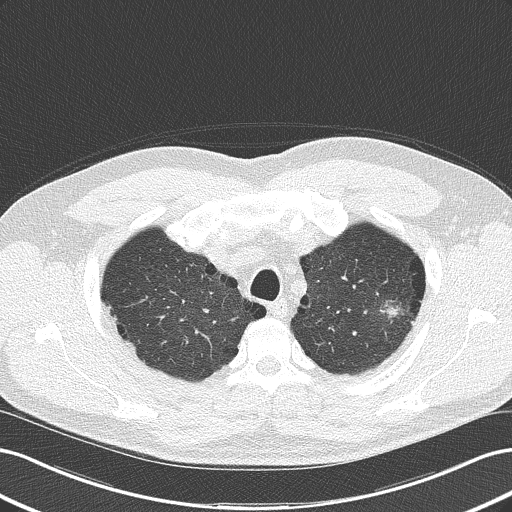
Chest CT (low-dose screening protocol), one axial image; second annual screen; lung window (W 1500 / L -600 HU); 2 mm slice thickness; 512 × 512 image matrix, field of view 360 × 360 mm. Male participant, aged 62 years at enrolment. Current smoker at enrolment.
- Lesion marked by an expert reader, box from (x=356, y=283) to (x=424, y=342) px.
- The screening reader recorded 2 non-calcified nodules or masses ≥4 mm on this exam; which of them this box marks is not recorded.
- Official screen result: positive, other.
- Later outcome: lung cancer diagnosed 46 days after this screen — adenocarcinoma, NOS, left upper lobe, well differentiated (G1), stage IB (AJCC 6th edition), 17 mm at pathology.